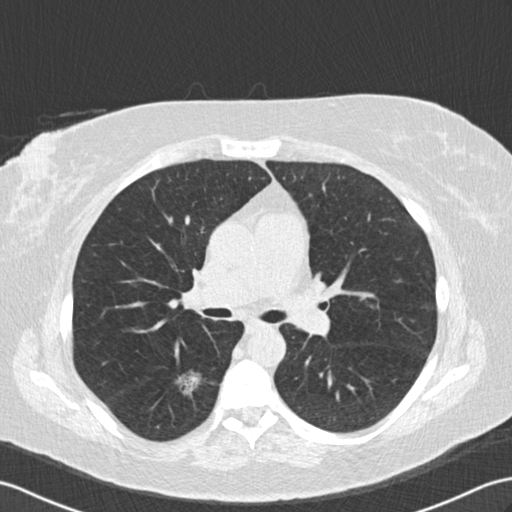
Low-dose screening chest CT, one axial slice; position 94 of 154 along the scan axis; reconstruction kernel B30f; 120 kVp; lung window (W 1500 / L -600 HU); 512 × 512 image matrix.
Structures marked on this image (expert manual segmentation):
- lesion 1 (tumor, lower lobe of right lung): bounding box <176,369,202,397> (left, top, right, bottom; pixels)